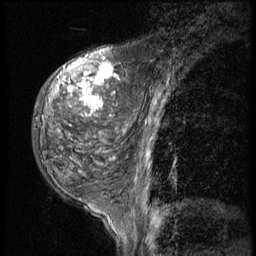
Breast MRI (dynamic contrast-enhanced), one sagittal slice. Slice 17 of 56 in the series (ordered by position). 3 images stored at this slice position (order not interpretable as contrast timing). 1.5 T. TE 4.2 ms, TR 9 ms. 2.5 mm slice thickness. 256 × 256 image matrix, field of view 180 × 180 mm. Female patient, age 50 years. From the clinical record (not read from this slice): setting: breast cancer imaged before/during neoadjuvant chemotherapy; receptor status: triple-negative.
Structures marked on this image (semi-automatic segmentation, software-assisted and operator-edited):
- analysis volume of interest (the breast-tissue region the enhancement analysis was run in; not a lesion): box from (x=31, y=50) to (x=116, y=191) px
- tumour enhancement mask (voxels above the 140 % enhancement threshold inside the analysis volume of interest): (x=67, y=65)–(x=116, y=160)